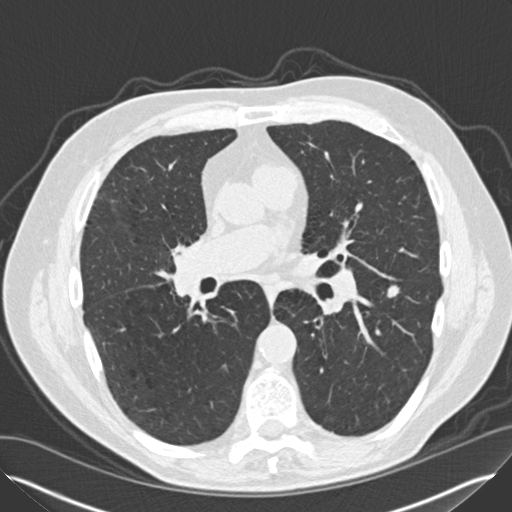
Low-dose screening chest CT, axial slice. Second screening round (one year after baseline). Lung window (W 1500 / L -600 HU). 2 mm slice thickness. Standard (soft-tissue) reconstruction kernel (B30f). Male, age 65 years at enrolment. Current smoker at enrolment.
Lesion marked by an expert reader, bounding box [x1, y1, x2, y2] px = [372, 276, 413, 312]. Screening reader's record for this exam (one nodule recorded; not confirmed to be the boxed lesion): non-calcified nodule or mass ≥4 mm, left lower lobe, 12 × 8 mm, smooth margins, soft tissue attenuation, pre-existing on the prior screen: yes; interval growth: yes. Official screen result: positive, other. Lung cancer was diagnosed 67 days after this screen: non-small cell carcinoma, left lower lobe, right hilum, poorly differentiated (G3), stage IV (AJCC 6th edition), 5 mm at pathology.